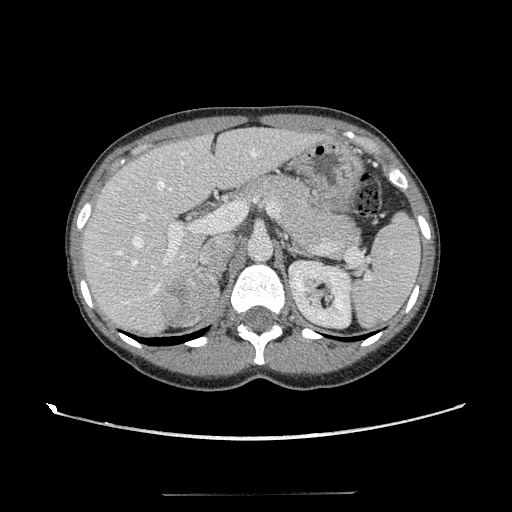
Contrast-enhanced abdominal CT, one axial slice; slice 74 of 117 in the series (ordered by position); reconstruction kernel STANDARD; 120 kVp; soft-tissue window (W 400 / L 40 HU); 2.5 mm slice thickness; 512 × 512 image matrix, field of view 365 × 365 mm. Patient: female, 35 years. From the clinical record (not read from this slice): diagnosis: adrenocortical carcinoma; tumour side: right adrenal; tumour size at pathology: 3 cm.
Outlined on this slice (semi-automatic segmentation, software-assisted and operator-edited):
- mass: bounding box (x1, y1, x2, y2) in pixels: (161, 276, 218, 325)